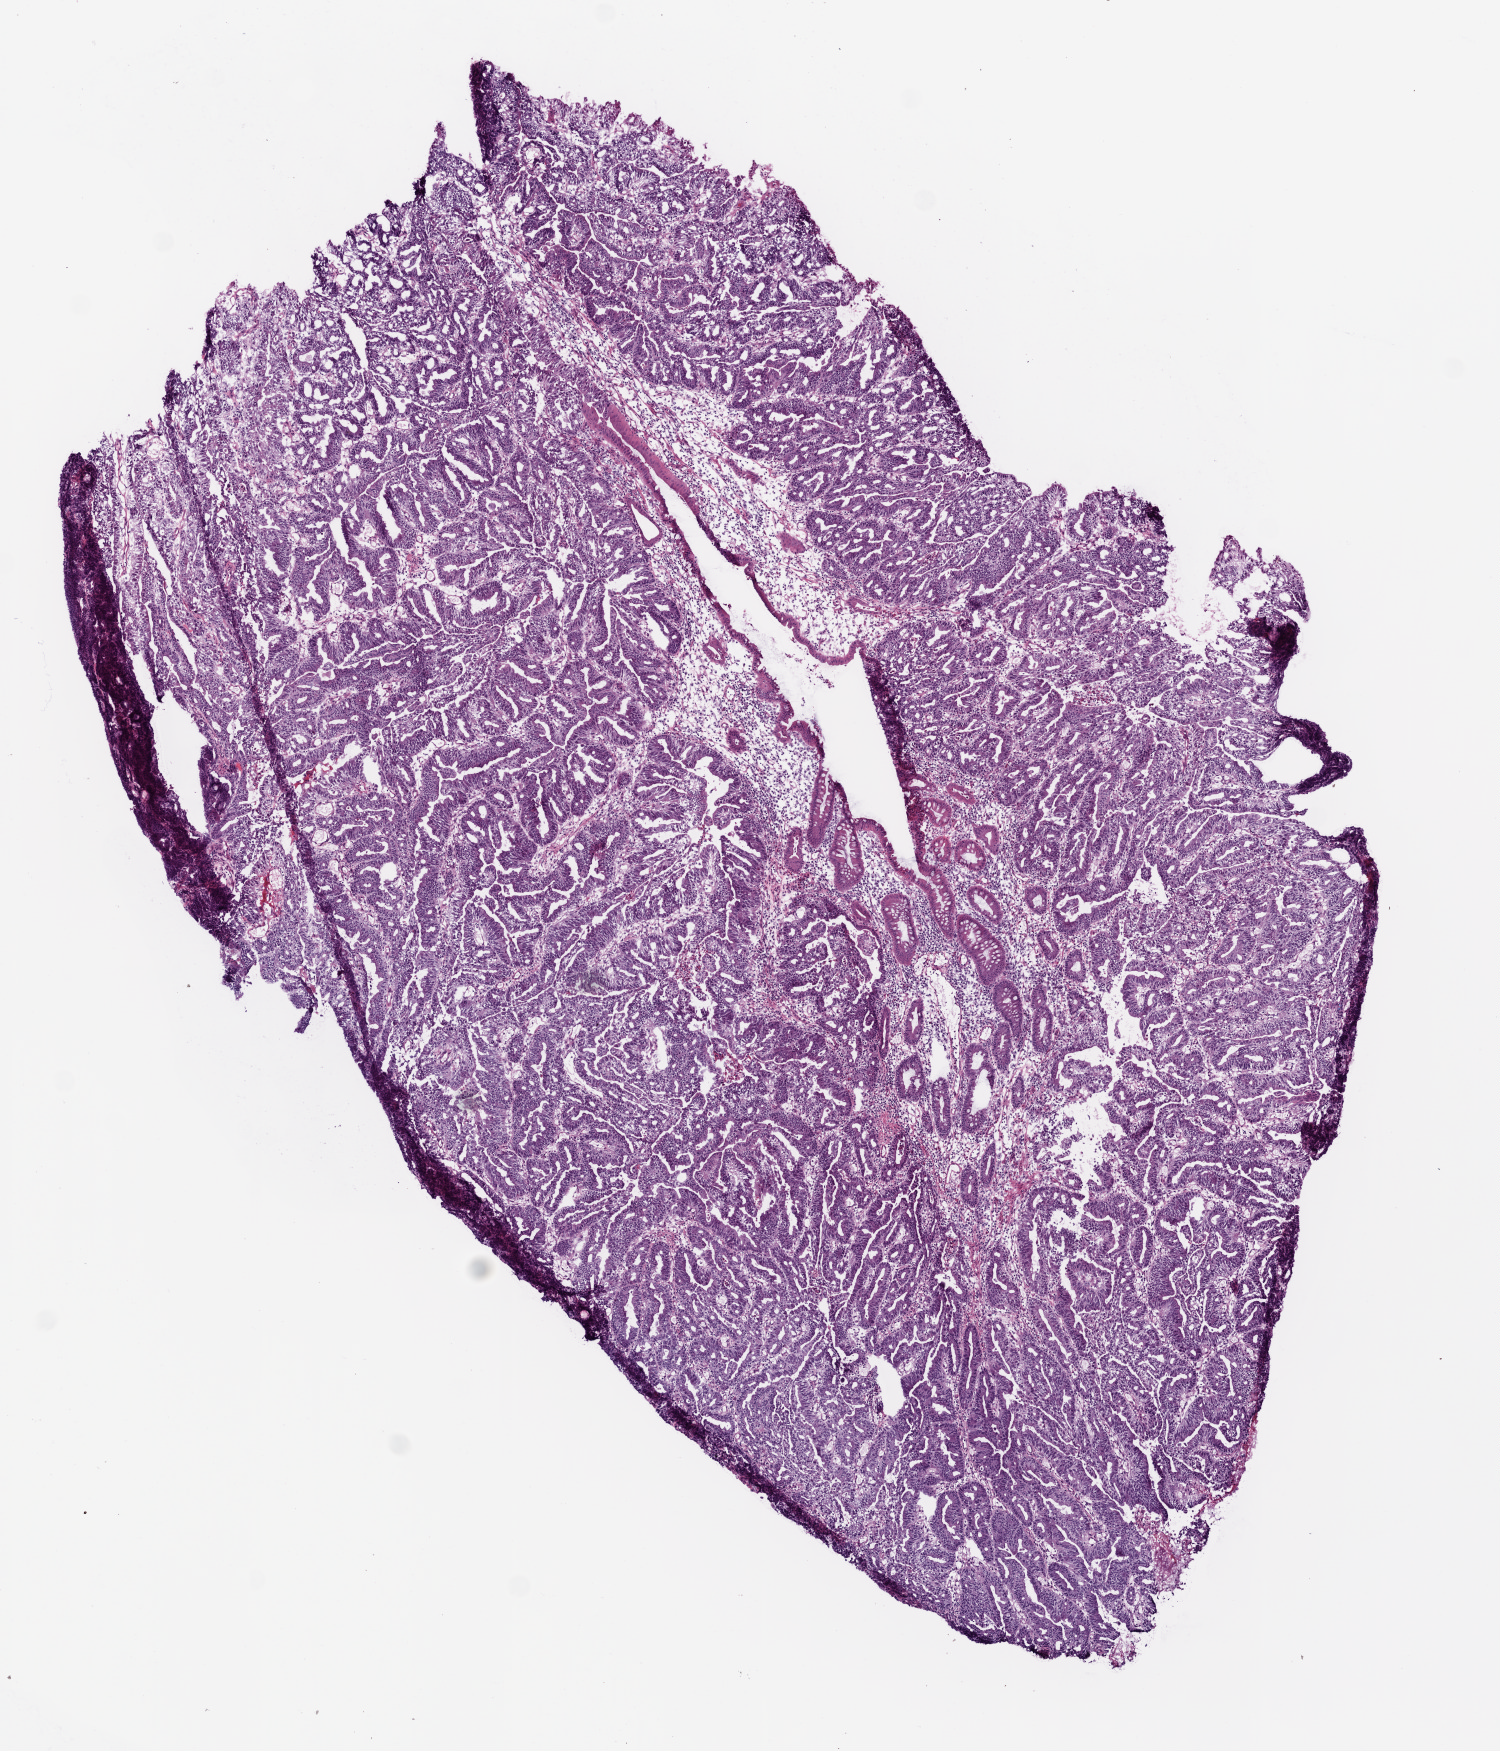
Hematoxylin and eosin (H&E) stained whole-slide image, low-resolution overview of the scanned area, about 6.0 x 7.0 mm (from a 20x scan). Frozen section from the top of the tissue portion. Sample: primary tumour, colon. Female patient; age at initial diagnosis 74 years. Slide review estimates, as recorded: tumour cells 100%, tumour nuclei 80%, normal cells 0%, stromal cells 0%, necrosis 0%. Inflammatory infiltration, as recorded: lymphocyte infiltration 40%, monocyte infiltration 5%, neutrophil infiltration 50%.
Lymph nodes positive (case pathology): 0 of 22 examined. AJCC pathologic stage: II (5th edition). Diagnosis: Adenocarcinoma, NOS (ascending colon).